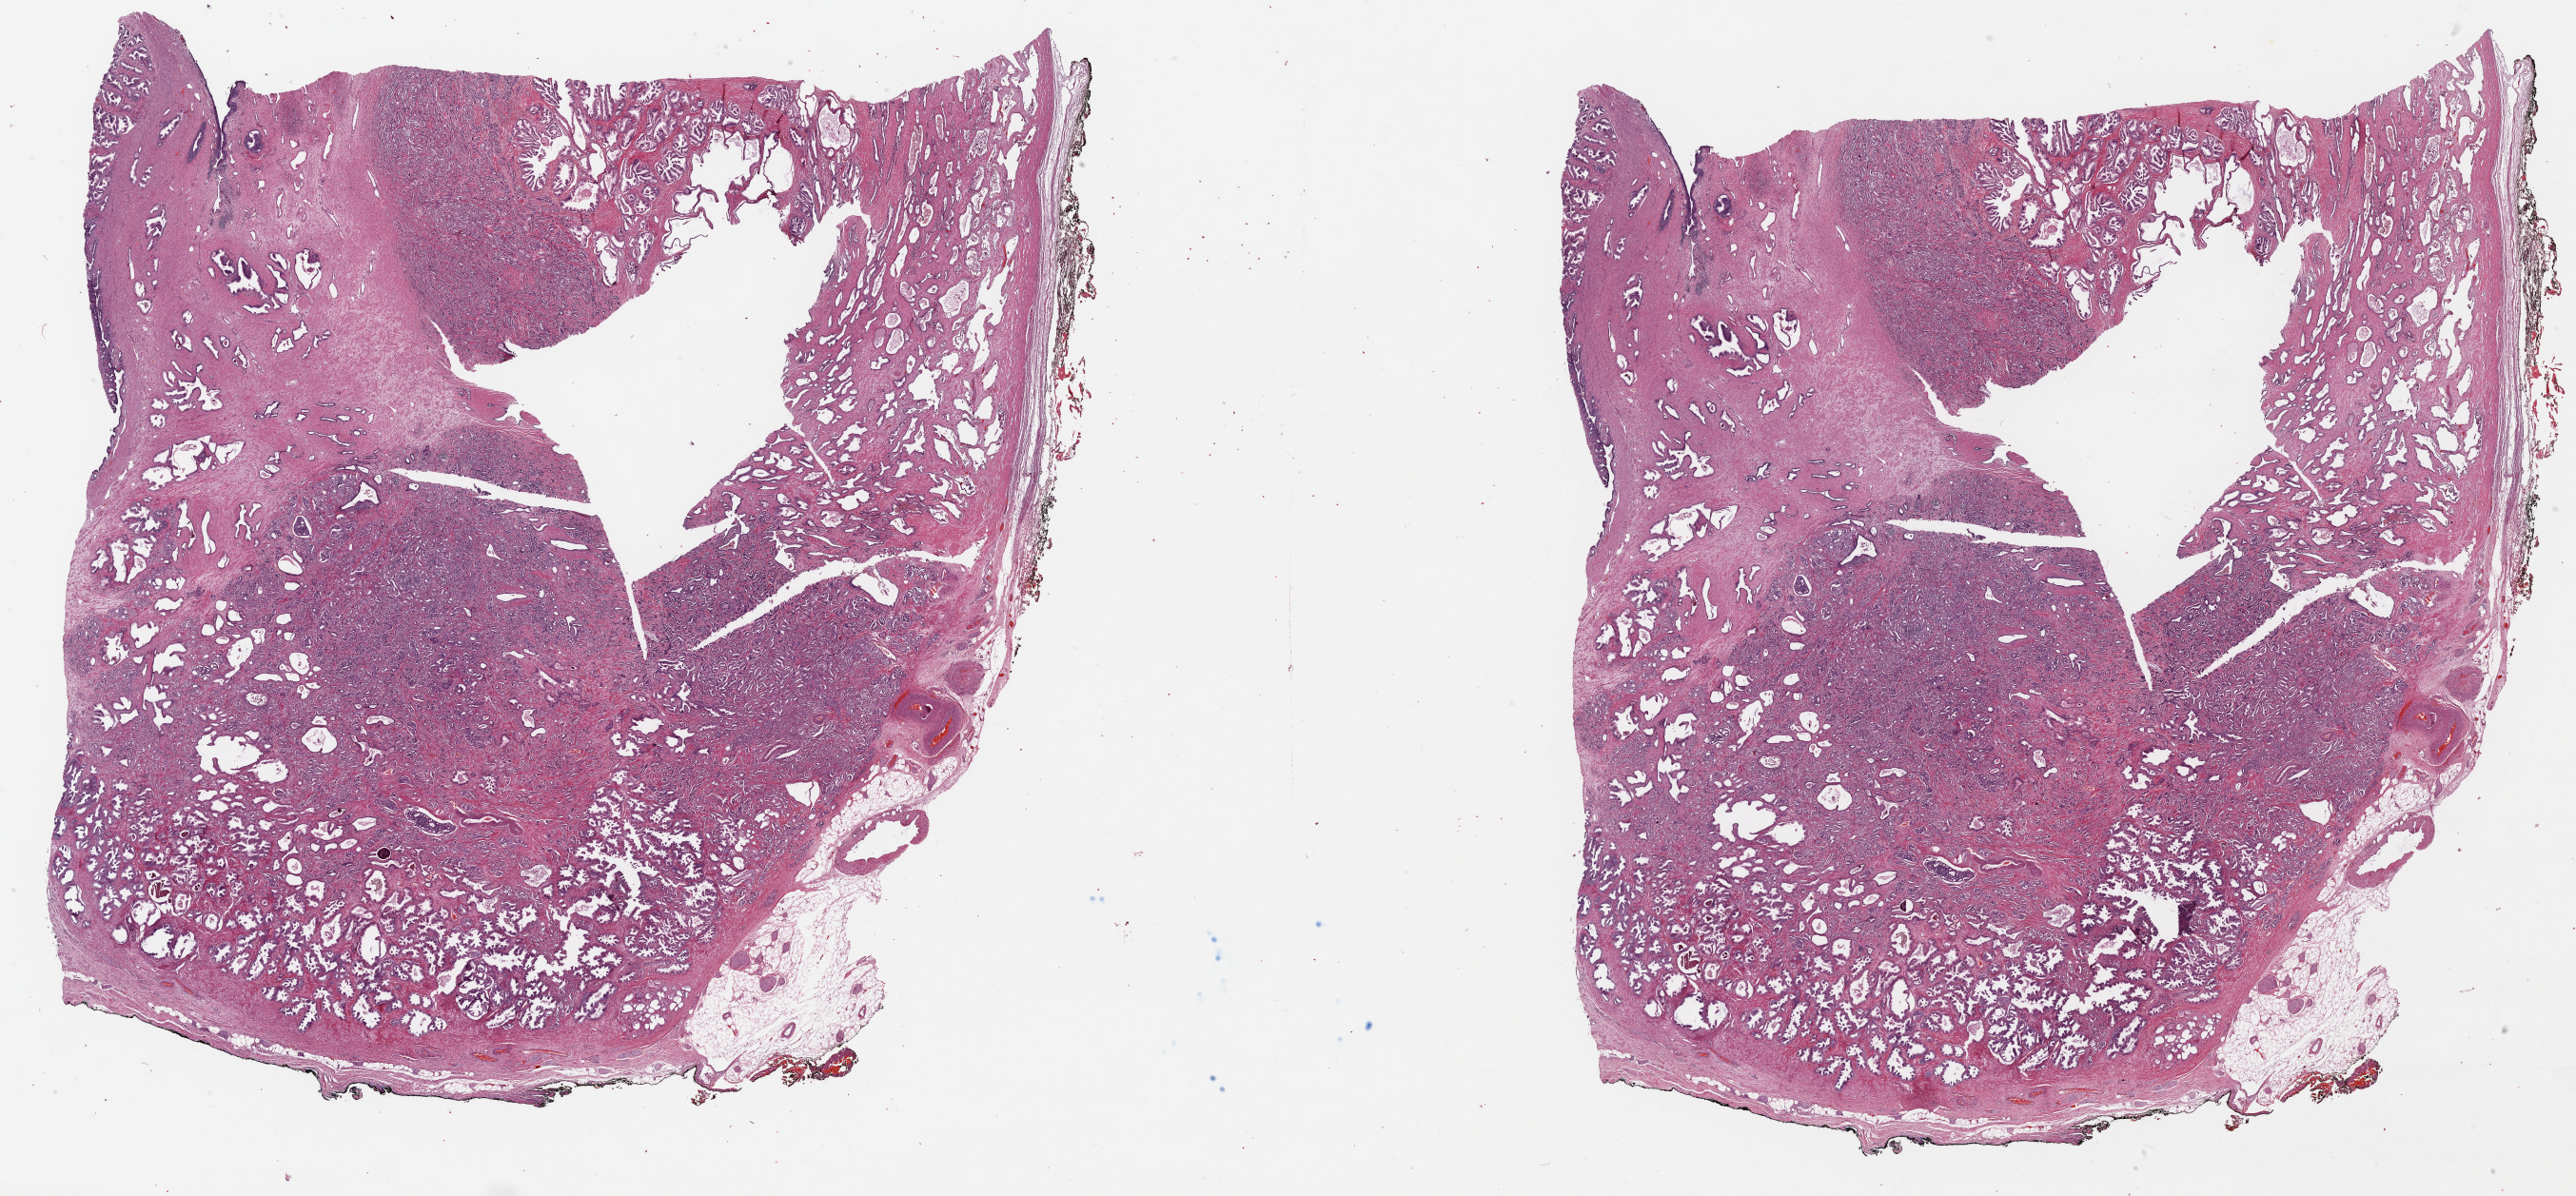
H&E-stained whole-slide image, shown as a low-resolution overview of the whole scanned area (about 42.6 x 19.8 mm, slide scanned at 40x). Formalin-fixed paraffin-embedded (FFPE) diagnostic section. Bladder, primary tumour sample. Patient: male, age at initial diagnosis 66 years. Histologic grade: high grade.
* AJCC pathologic stage: III (7th edition)
* histologic diagnosis: Transitional cell carcinoma
* lymph nodes positive (case pathology): 0 of 6 examined